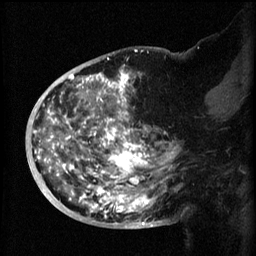
Breast MRI (dynamic contrast-enhanced), one sagittal slice. Position 32 of 60 along the scan axis. 3 images stored at this slice position (order not interpretable as contrast timing). 1.5 T. TE 4.2 ms, TR 8.2 ms. 2 mm slice thickness. 256 × 256 image matrix, field of view 200 × 200 mm. Female patient, age 50 years.
Structures marked on this image (semi-automatically segmented with operator editing):
- analysis volume of interest (the breast-tissue region the enhancement analysis was run in; not a lesion): bounding box [x1, y1, x2, y2] px = [44, 72, 173, 219]
- tumour enhancement mask (voxels above the 70 % enhancement threshold inside the analysis volume of interest): [44, 72, 173, 219]